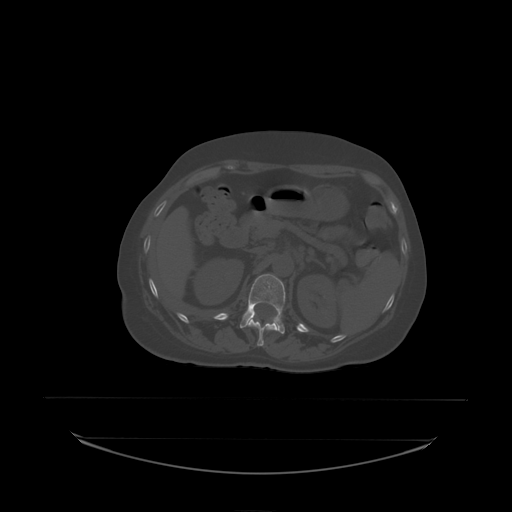
CT including the spine, one axial slice; position 87 of 242 along the scan axis; bone window (W 1800 / L 400 HU); 512 × 512 image matrix, field of view 500 × 500 mm. Female patient, age 53 years. Case-level facts recorded for this patient, not image findings: primary cancer: lung; vertebrae with lytic lesions (as recorded): T7, L1.
Annotated regions visible in this slice (semi-automatic segmentation, software-assisted and operator-edited):
- L1 vertebra: bounding box <240,274,286,334> (left, top, right, bottom; pixels)
- T12 vertebra: <248,318,278,338>